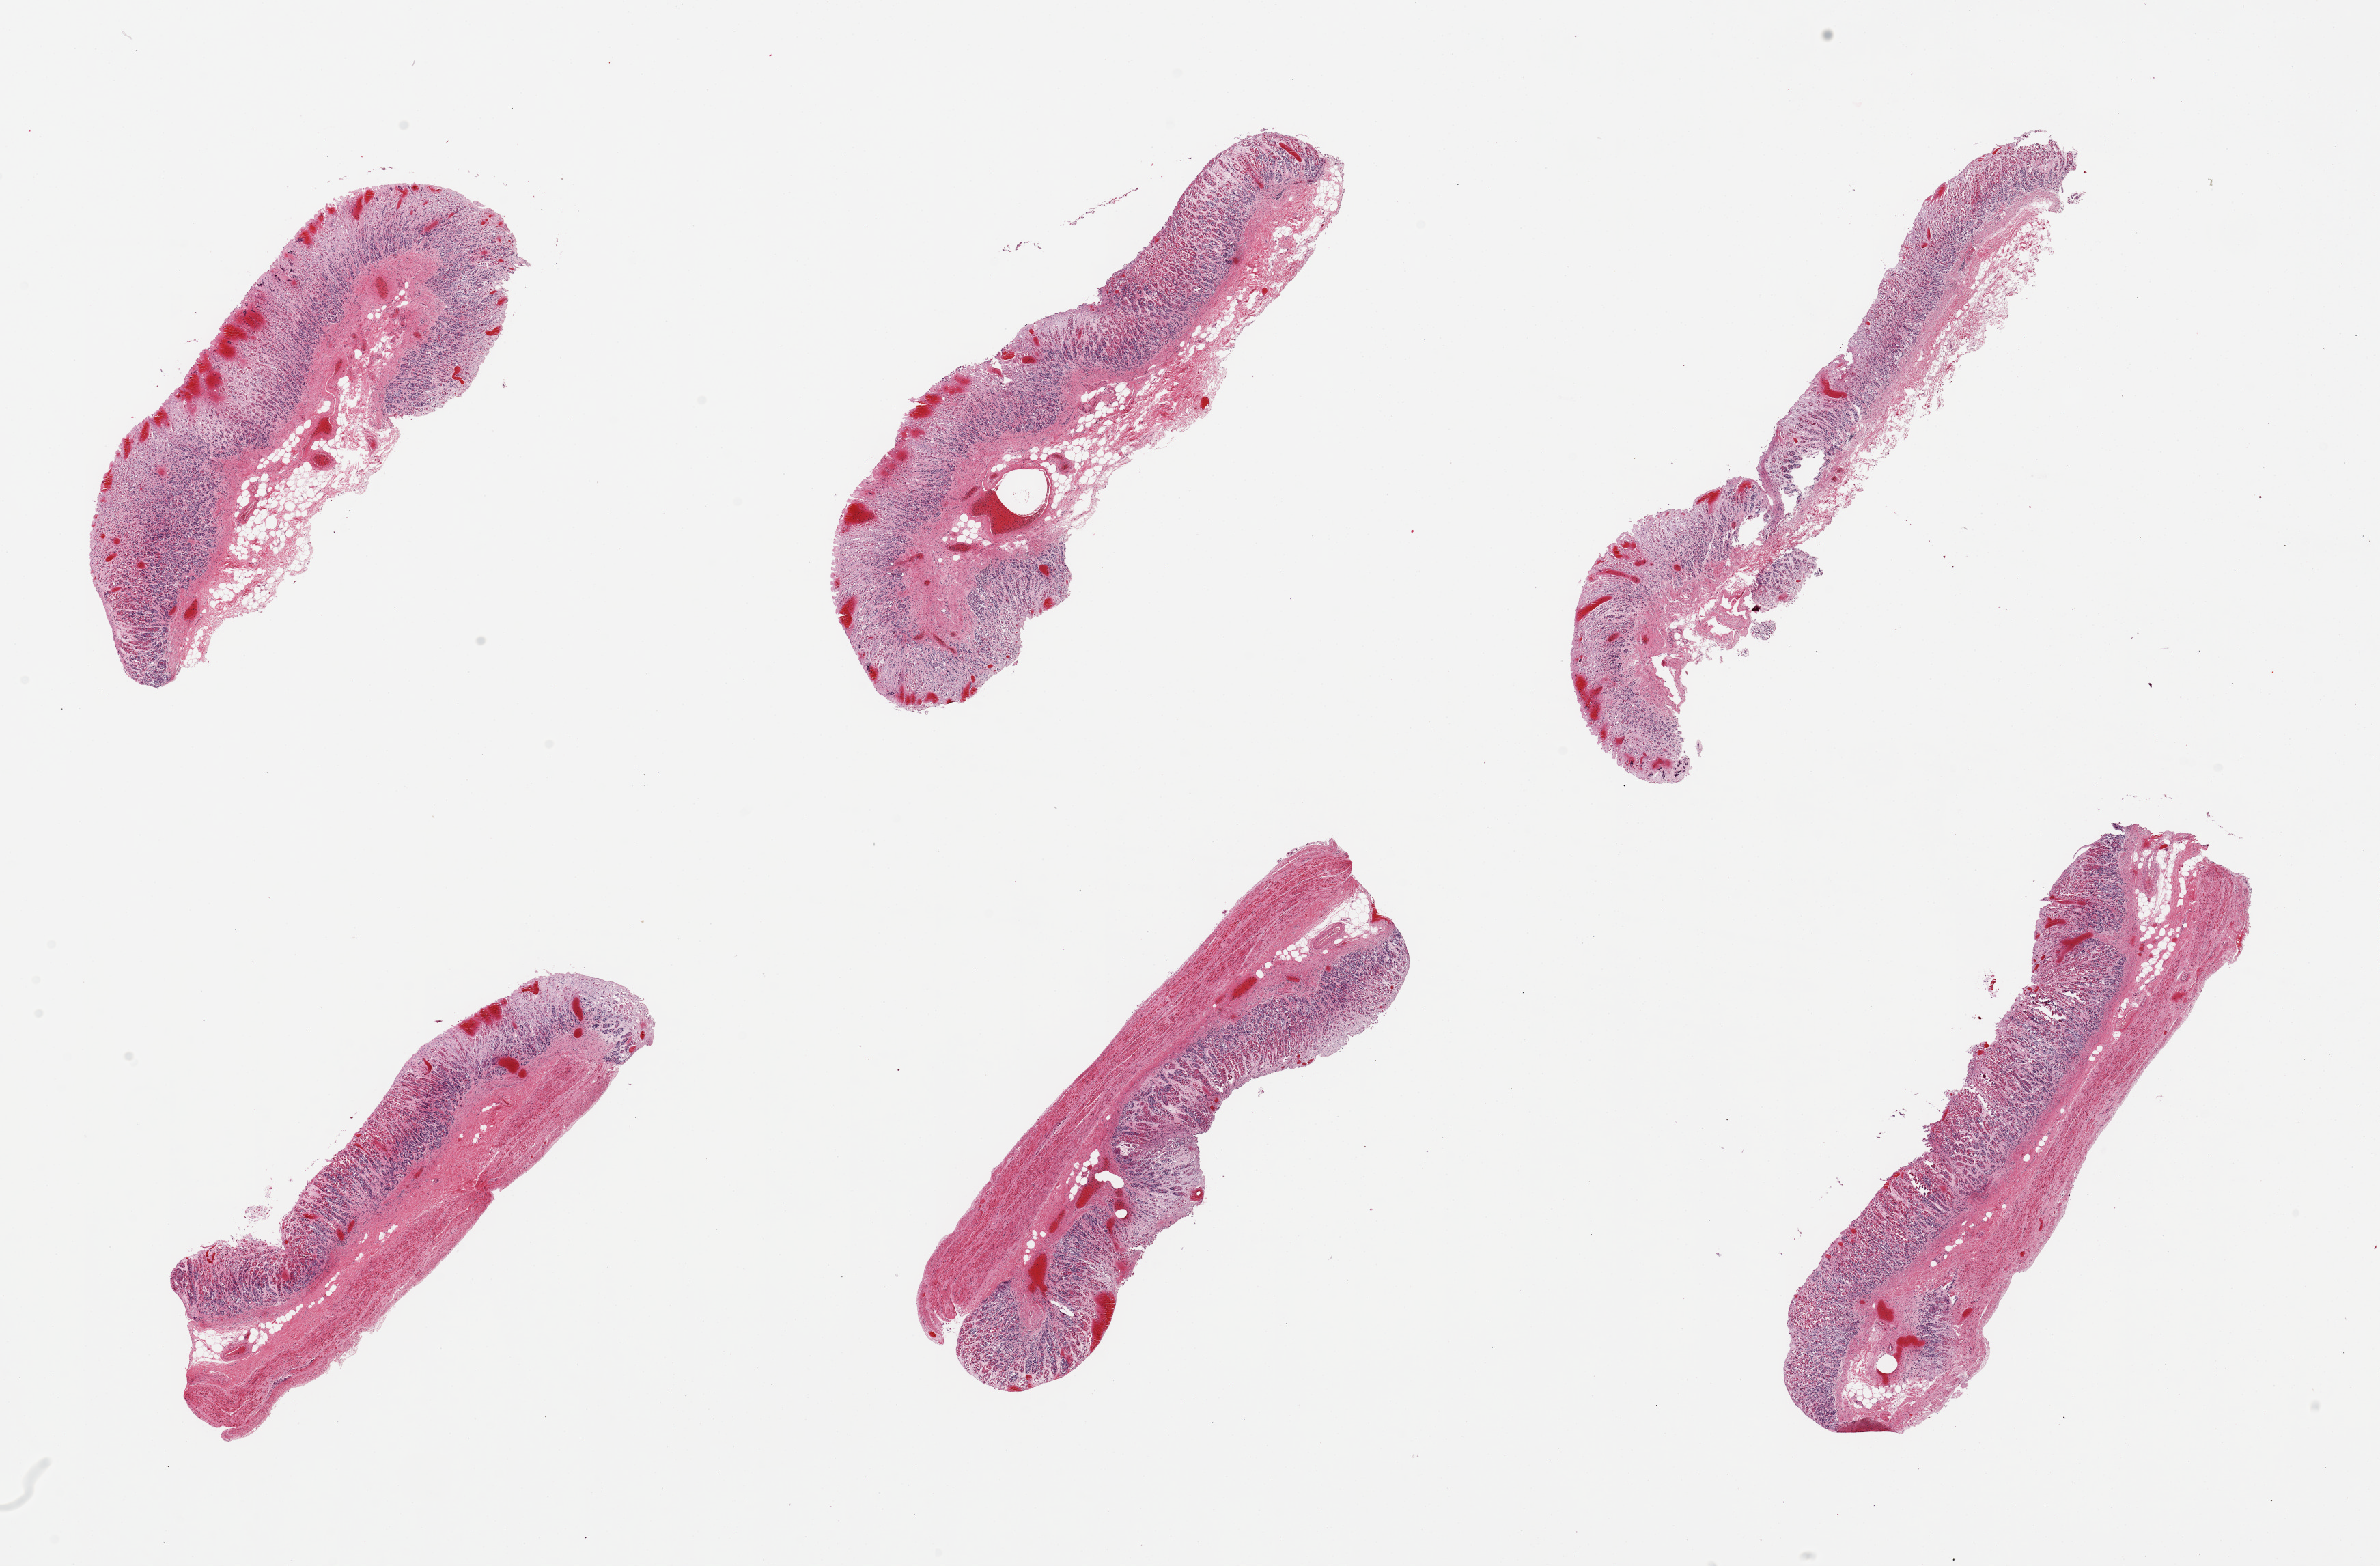
H&E whole-slide image, whole scanned area (about 27.6 x 18.1 mm, acquisition: 20x scan) shown as a low-resolution overview, PAXgene-fixed paraffin-embedded (PFPE) section, section of stomach (target tissue), tissue donor sample. Donor: male.
Review note (as recorded): 6 pieces, mucosa up to ~50% thickness, but badly autolyzed. Evidence of diffuse antemortem/perimortem hemorrhagic event. Intramucosal findings suggest component of pill gastrtitis, too autolyzed for further assessment.